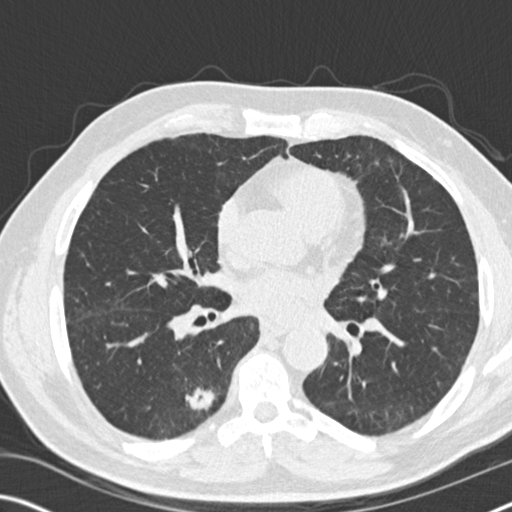
Chest CT (low-dose screening protocol), one axial image. Baseline annual screen. Lung window (W 1500 / L -600 HU). Slice 86 of 169 in the series. Male participant, aged 71 years at enrolment.
• Lesion marked by an expert reader, bounding box [x1, y1, x2, y2] px = [160, 371, 229, 433].
• The screening reader recorded 2 non-calcified nodules or masses ≥4 mm on this exam; which of them this box marks is not recorded.
• Participant outcome: lung cancer diagnosed 215 days after this screen — squamous cell carcinoma, NOS, right lower lobe, moderately differentiated (G2), stage IB (AJCC 6th edition), 52 mm at pathology.